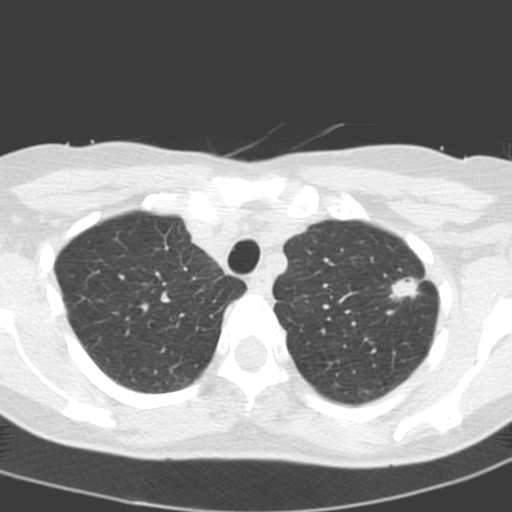
Low-dose screening chest CT, one axial slice; position 158 of 193 along the scan axis; 120 kVp; lung window (W 1500 / L -600 HU); 512 × 512 image matrix.
Outlined on this slice (outlined manually by an expert reader):
- lesion 1 (tumor, upper lobe of left lung): box from (x=390, y=277) to (x=420, y=300) px